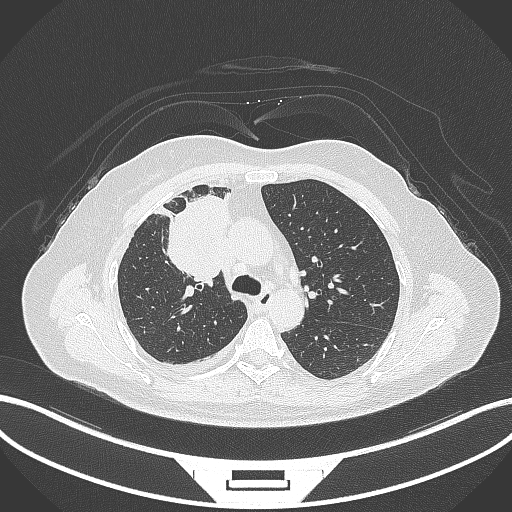
Chest CT, one axial slice; position 193 of 305 along the scan axis; 120 kVp; lung window (W 1500 / L -600 HU); 1 mm slice thickness; 512 × 512 image matrix. Patient: female, 52 years. Case-level facts recorded for this patient, not image findings: clinical TNM (as recorded): T3 N1 M1.
Structures marked on this image (rectangle marked by the reading radiologist):
- lung tumour (recorded histology: adenocarcinoma): box from (x=159, y=186) to (x=237, y=282) px